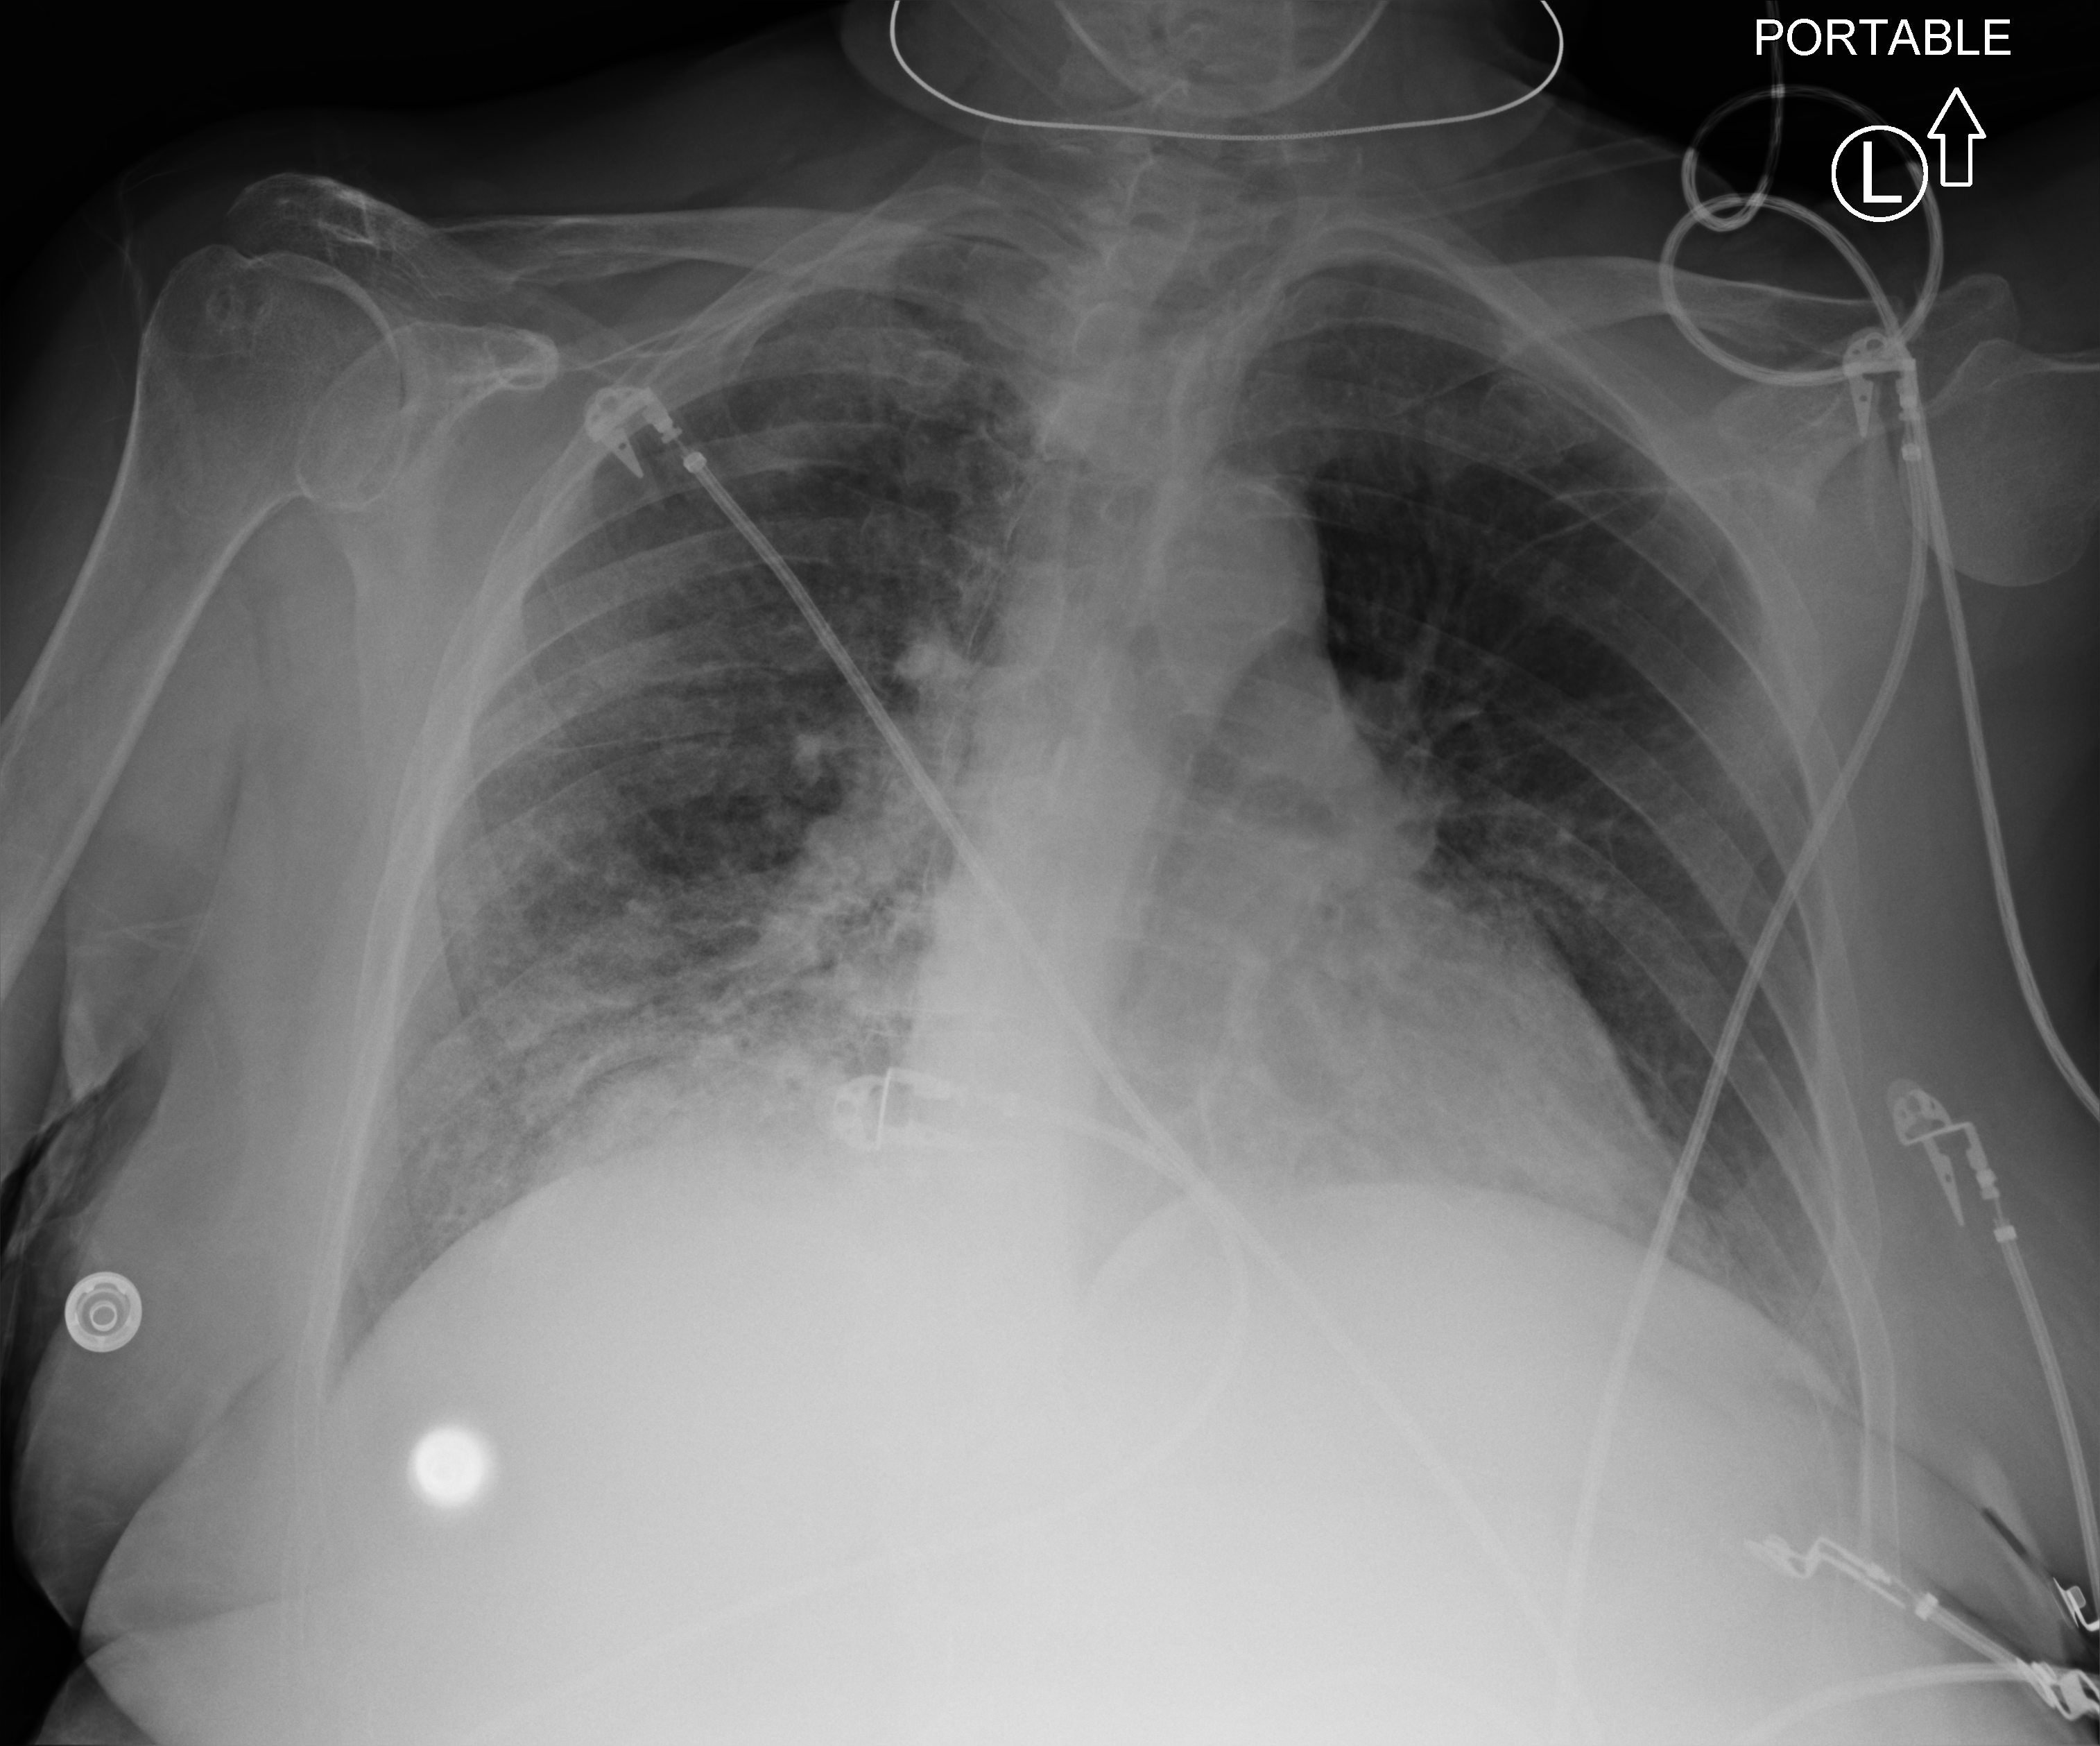
Portable chest radiograph; anteroposterior (AP) projection. Patient hospitalised with COVID-19; female, aged 75–90 years.
From the hospital-stay record, not from the radiograph (when in the stay this image was taken is not recorded): admitted to intensive care during this hospital stay: yes; length of hospital stay: 28 days.